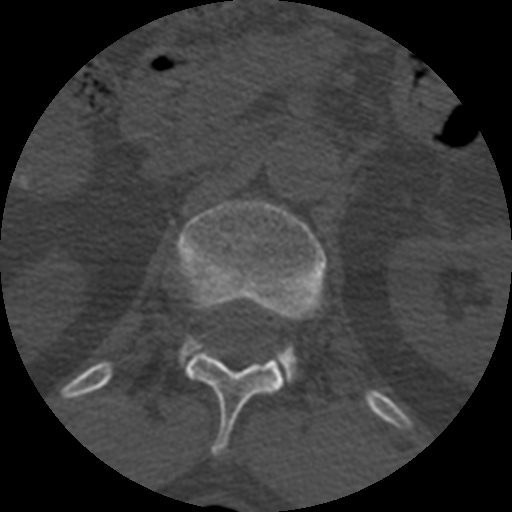
CT including the spine, one axial slice. Slice 375 of 399 in the series (ordered by position). Reconstruction kernel STANDARD. 120 kVp. Bone window (W 1800 / L 400 HU). 512 × 512 image matrix, field of view 160 × 160 mm. Patient age 71 years. Case-level facts recorded for this patient, not image findings: primary cancer: prostate.
Annotated regions visible in this slice (semi-automatic segmentation, software-assisted and operator-edited):
- L1 vertebra: bounding box [x1, y1, x2, y2] px = [177, 199, 325, 384]
- T12 vertebra: [181, 346, 284, 458]